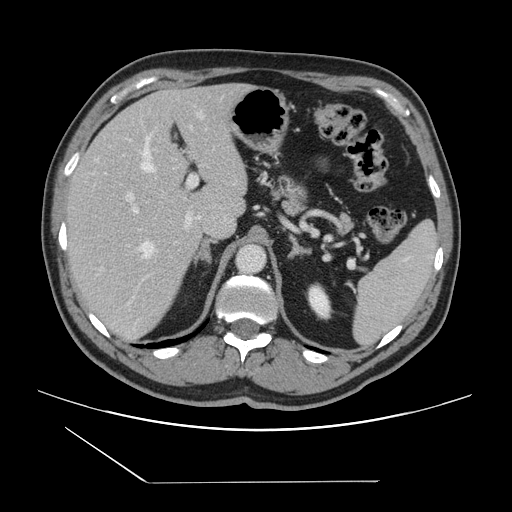
Contrast-enhanced abdominal CT, one axial slice; position 95 of 157 along the scan axis; 120 kVp; soft-tissue window (W 400 / L 40 HU); 2.5 mm slice thickness; 512 × 512 image matrix, field of view 407 × 407 mm. Male patient, age 61 years. Case-level facts recorded for this patient, not image findings: diagnosis: colorectal cancer liver metastases, imaged before liver resection; multiple liver metastases: yes; largest metastasis: 5.5 cm; disease in both lobes: yes.
Outlined on this slice (outlined manually by an expert reader):
- hepatic veins: box from (x=140, y=114) to (x=203, y=257) px
- liver: (x=65, y=85)–(x=248, y=341)
- planned liver remnant (the part of the liver to remain after resection): (x=67, y=85)–(x=238, y=223)
- portal vein (with intrahepatic branches): (x=102, y=174)–(x=201, y=270)